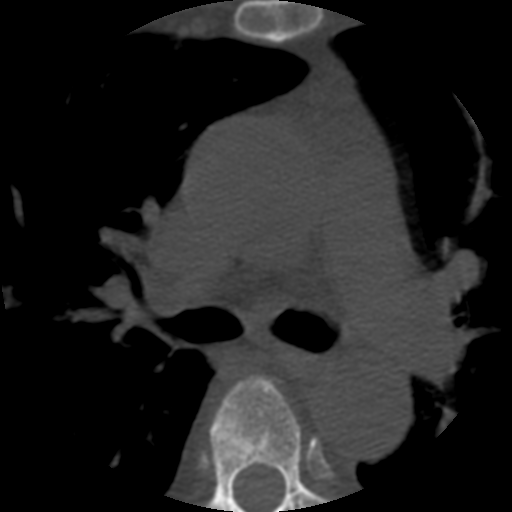
CT including the spine, one axial slice; position 378 of 508 along the scan axis; reconstruction kernel STANDARD; bone window (W 1800 / L 400 HU); 512 × 512 image matrix, field of view 160 × 160 mm. Patient age 57 years. From the clinical record (not read from this slice): primary cancer: prostate.
Structures marked on this image (semi-automatic segmentation, software-assisted and operator-edited):
- T5 vertebra: bounding box (x1, y1, x2, y2) in pixels: (208, 377, 323, 512)